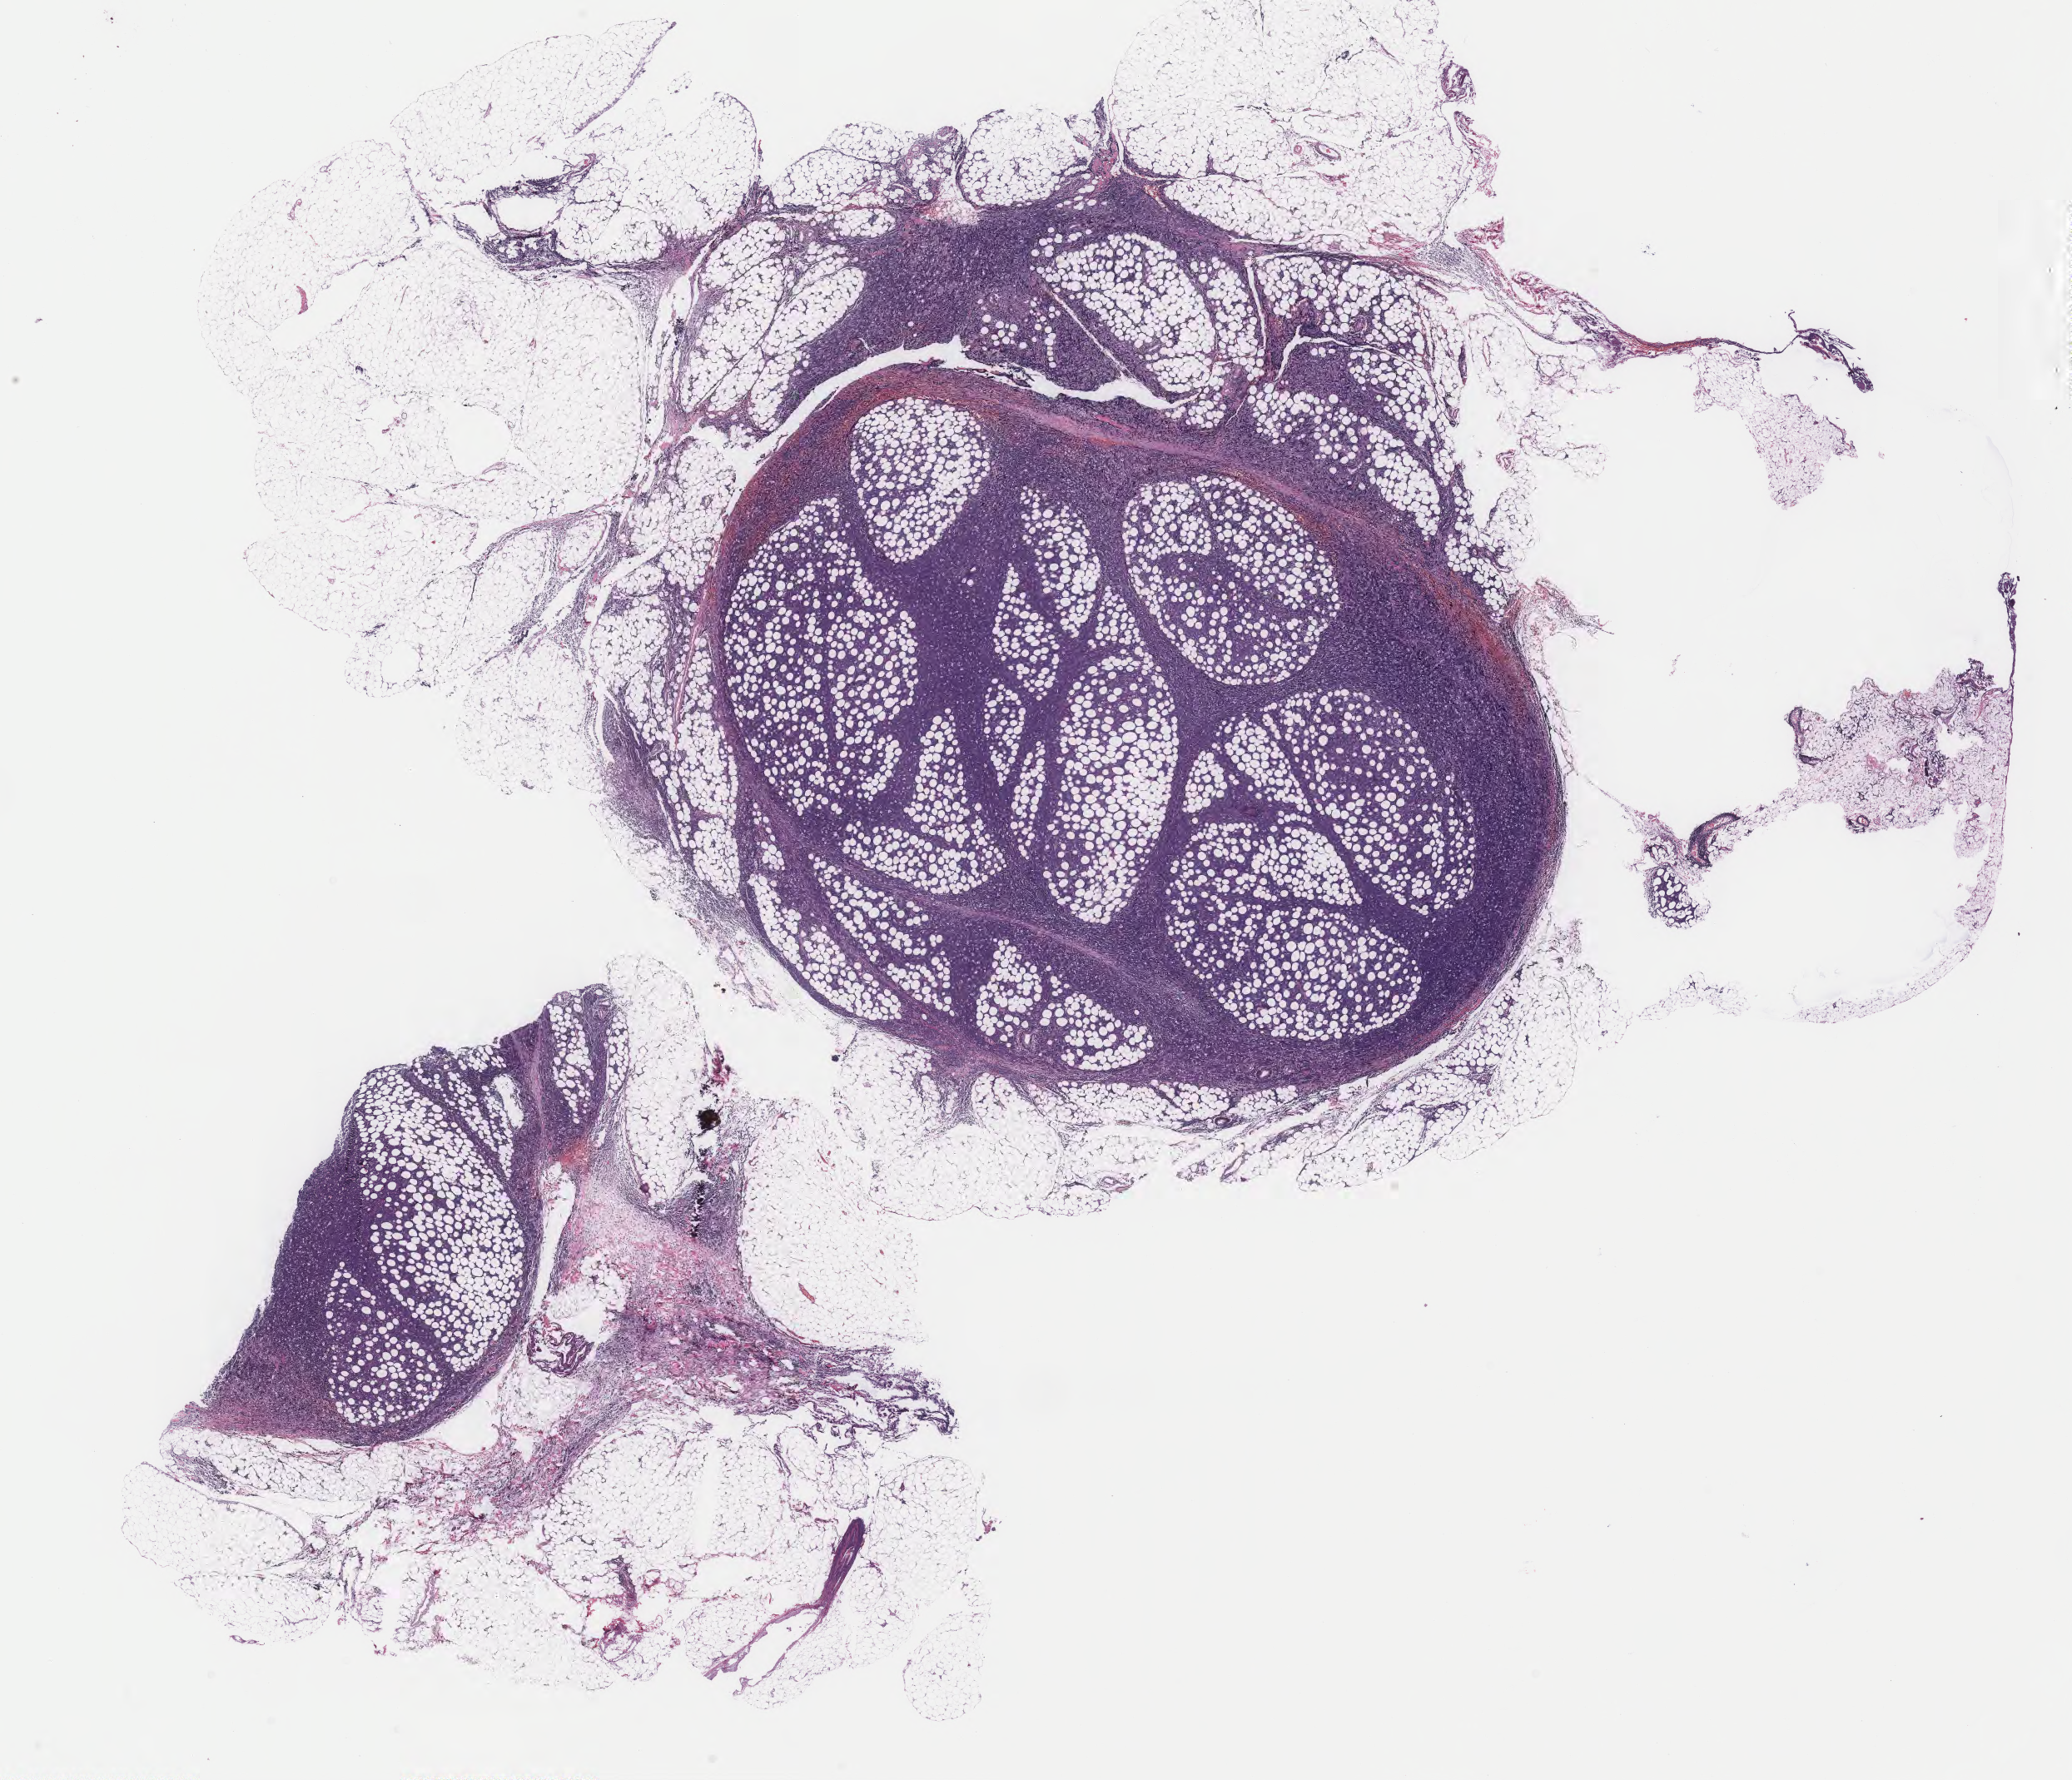
Digitized haematoxylin and eosin-stained section, whole scanned area (about 19.7 x 16.9 mm) shown as a low-resolution overview. Formalin-fixed, paraffin-embedded (FFPE) tissue. Specimen: primary tumor. Patient: male, age 24 years. Slide review estimates, as recorded: tumor cells 70%, tumor nuclei 95%, stromal cells 25%, necrosis 5%, normal cells 0%. Inflammatory infiltration, as recorded: lymphocyte infiltration 40%, monocyte infiltration 20%, neutrophil infiltration 5%.
Ann Arbor stage (patient): Stage IV. Section: top of the tissue portion. Histologic diagnosis: Burkitt lymphoma, NOS.